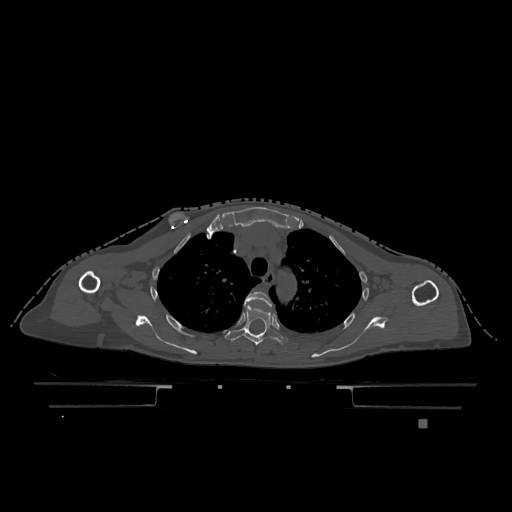
CT including the spine, one axial slice; position 890 of 1317 along the scan axis; bone window (W 1800 / L 400 HU); 512 × 512 image matrix. Patient: female, 74 years. From the clinical record (not read from this slice): primary cancer: lung.
Outlined on this slice (semi-automatically segmented with operator editing):
- T3 vertebra: bounding box [x1, y1, x2, y2] px = [245, 291, 272, 306]
- T4 vertebra: [224, 305, 288, 345]